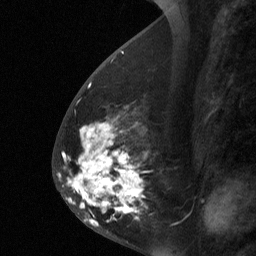
Breast MRI (dynamic contrast-enhanced), one sagittal slice; position 26 of 64 along the scan axis; dynamic contrast-enhanced study with each time point stored as its own series, time point 2 of 3 at this slice position (early post-contrast, ordered by acquisition time); 1.5 T; TE 4.8 ms, TR 27 ms; 2 mm slice thickness; 256 × 256 image matrix. Patient: female, 56 years. Case-level facts recorded for this patient, not image findings: setting: breast cancer imaged before/during neoadjuvant chemotherapy; receptor status: HER2-positive.
Outlined on this slice (semi-automatically segmented with operator editing):
- analysis volume of interest (the breast-tissue region the enhancement analysis was run in; not a lesion): bounding box (x1, y1, x2, y2) in pixels: (59, 104, 148, 229)
- tumour enhancement mask (voxels above the 90 % enhancement threshold inside the analysis volume of interest): (59, 148, 142, 226)